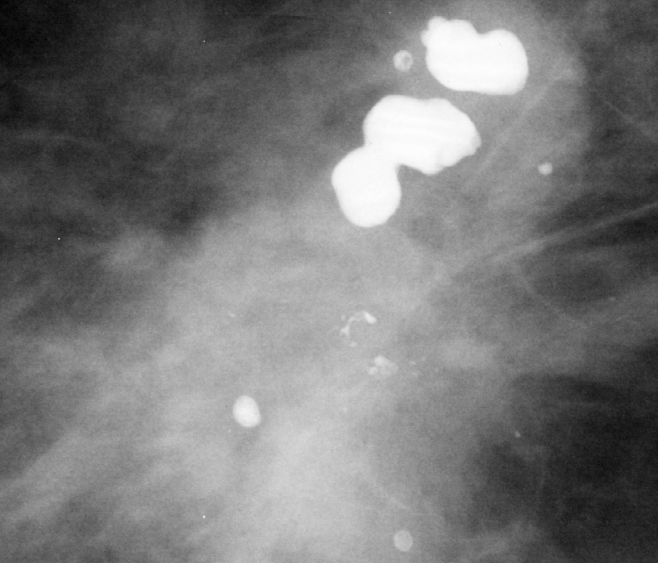
Crop from a digitized film mammogram around one marked abnormality; right breast; CC view.
- Finding: mass, shape architectural distortion, margins spiculated; BI-RADS assessment category 4; pathology (as recorded): malignant.